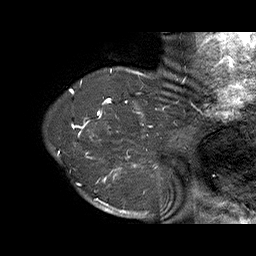
Breast MRI (dynamic contrast-enhanced), one sagittal slice; slice 61 of 70 in the series (ordered by position); dynamic contrast-enhanced series, time point 2 of 6 at this slice position (early post-contrast); 1.5 T; TE 4.5 ms, TR 32.4 ms; 3 mm slice thickness; 256 × 256 image matrix. Female patient. Case-level facts recorded for this patient, not image findings: setting: breast cancer imaged before/during neoadjuvant chemotherapy; receptor status: HR-positive, HER2-negative.
Structures marked on this image (semi-automatic segmentation, software-assisted and operator-edited):
- analysis volume of interest (the breast-tissue region the enhancement analysis was run in; not a lesion): box from (x=71, y=128) to (x=159, y=202) px
- tumour enhancement mask (voxels above the 100 % enhancement threshold inside the analysis volume of interest): (x=73, y=128)–(x=158, y=202)